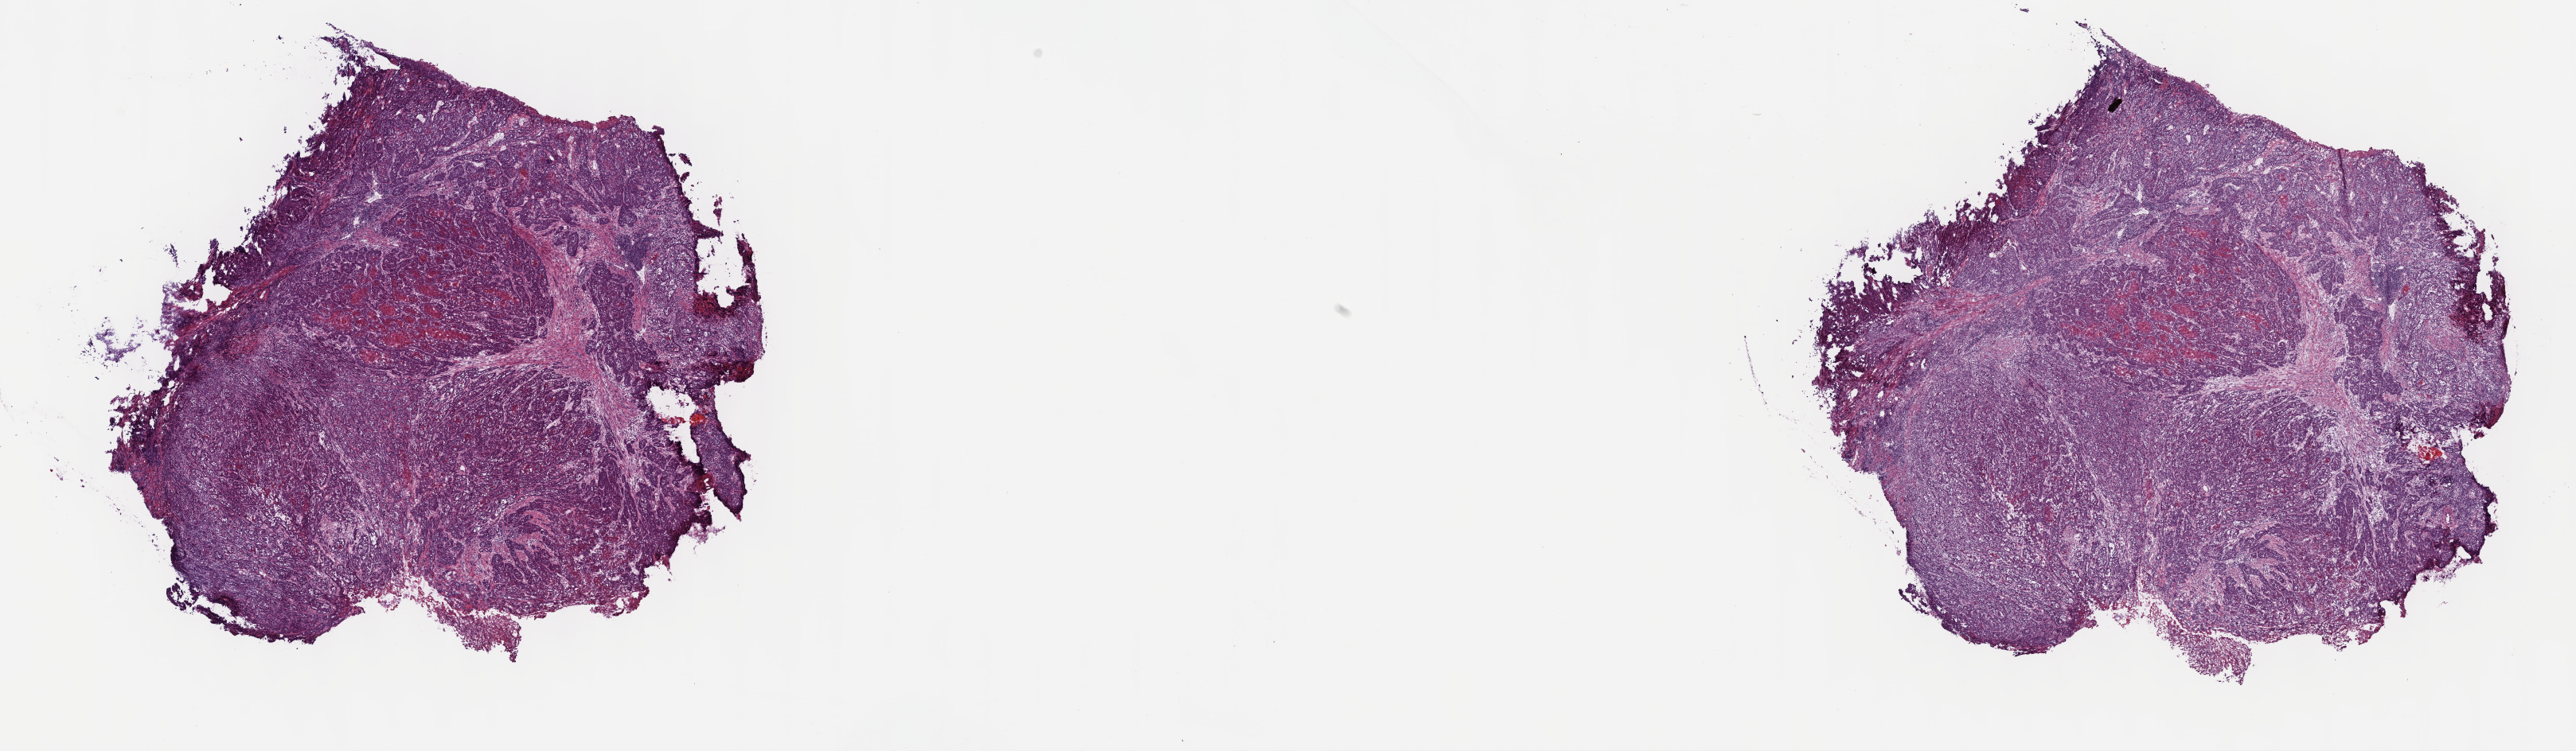
Whole-slide histology image, Hematoxylin and eosin (H&E) stained — shown as a low-resolution overview of the whole scanned area (about 26.2 x 7.6 mm, acquisition: 40x scan). Frozen section from the top of the tissue portion. Sample: primary tumour, esophagus. Male, age 58 years at initial diagnosis. Histologic grade: G2 (moderately differentiated). Slide review estimates, as recorded: tumour cells 100%, tumour nuclei 80%, normal cells 0%, stromal cells 0%, necrosis 0%. Inflammatory infiltration, as recorded: lymphocyte infiltration 0%, monocyte infiltration 0%, neutrophil infiltration 0%.
• diagnosis: Squamous cell carcinoma, NOS (middle third of esophagus)
• AJCC pathologic stage: IIIC